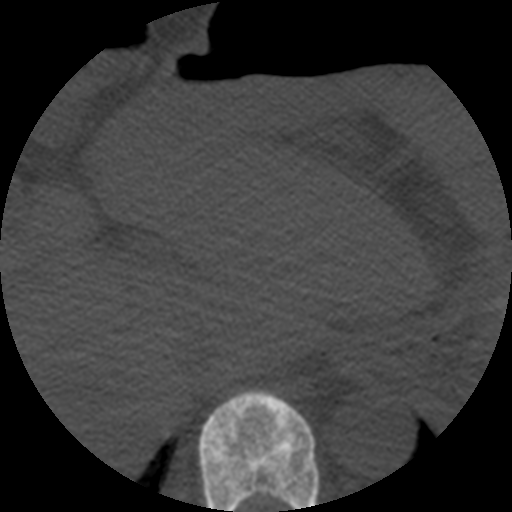
CT including the spine, one axial slice. Position 264 of 508 along the scan axis. Reconstruction kernel STANDARD. Bone window (W 1800 / L 400 HU). 1.25 mm slice thickness. 512 × 512 image matrix, field of view 160 × 160 mm. Patient age 57 years. Case-level facts recorded for this patient, not image findings: primary cancer: prostate.
Structures marked on this image (semi-automatically segmented with operator editing):
- T10 vertebra: bounding box [x1, y1, x2, y2] px = [198, 389, 320, 512]